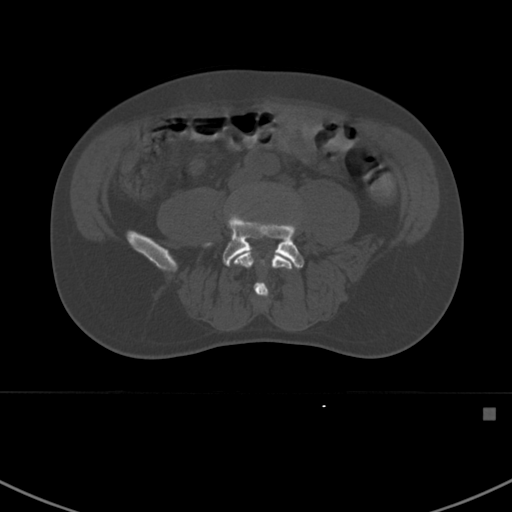
CT including the spine, one axial slice; slice 229 of 412 in the series (ordered by position); reconstruction kernel Br40s; bone window (W 1800 / L 400 HU); 1.5 mm slice thickness; 512 × 512 image matrix. Patient: male, 59 years. Case-level facts recorded for this patient, not image findings: primary cancer: prostate.
Structures marked on this image (semi-automatically segmented with operator editing):
- L4 vertebra: bounding box [x1, y1, x2, y2] px = [234, 249, 293, 298]
- L5 vertebra: [206, 213, 304, 269]